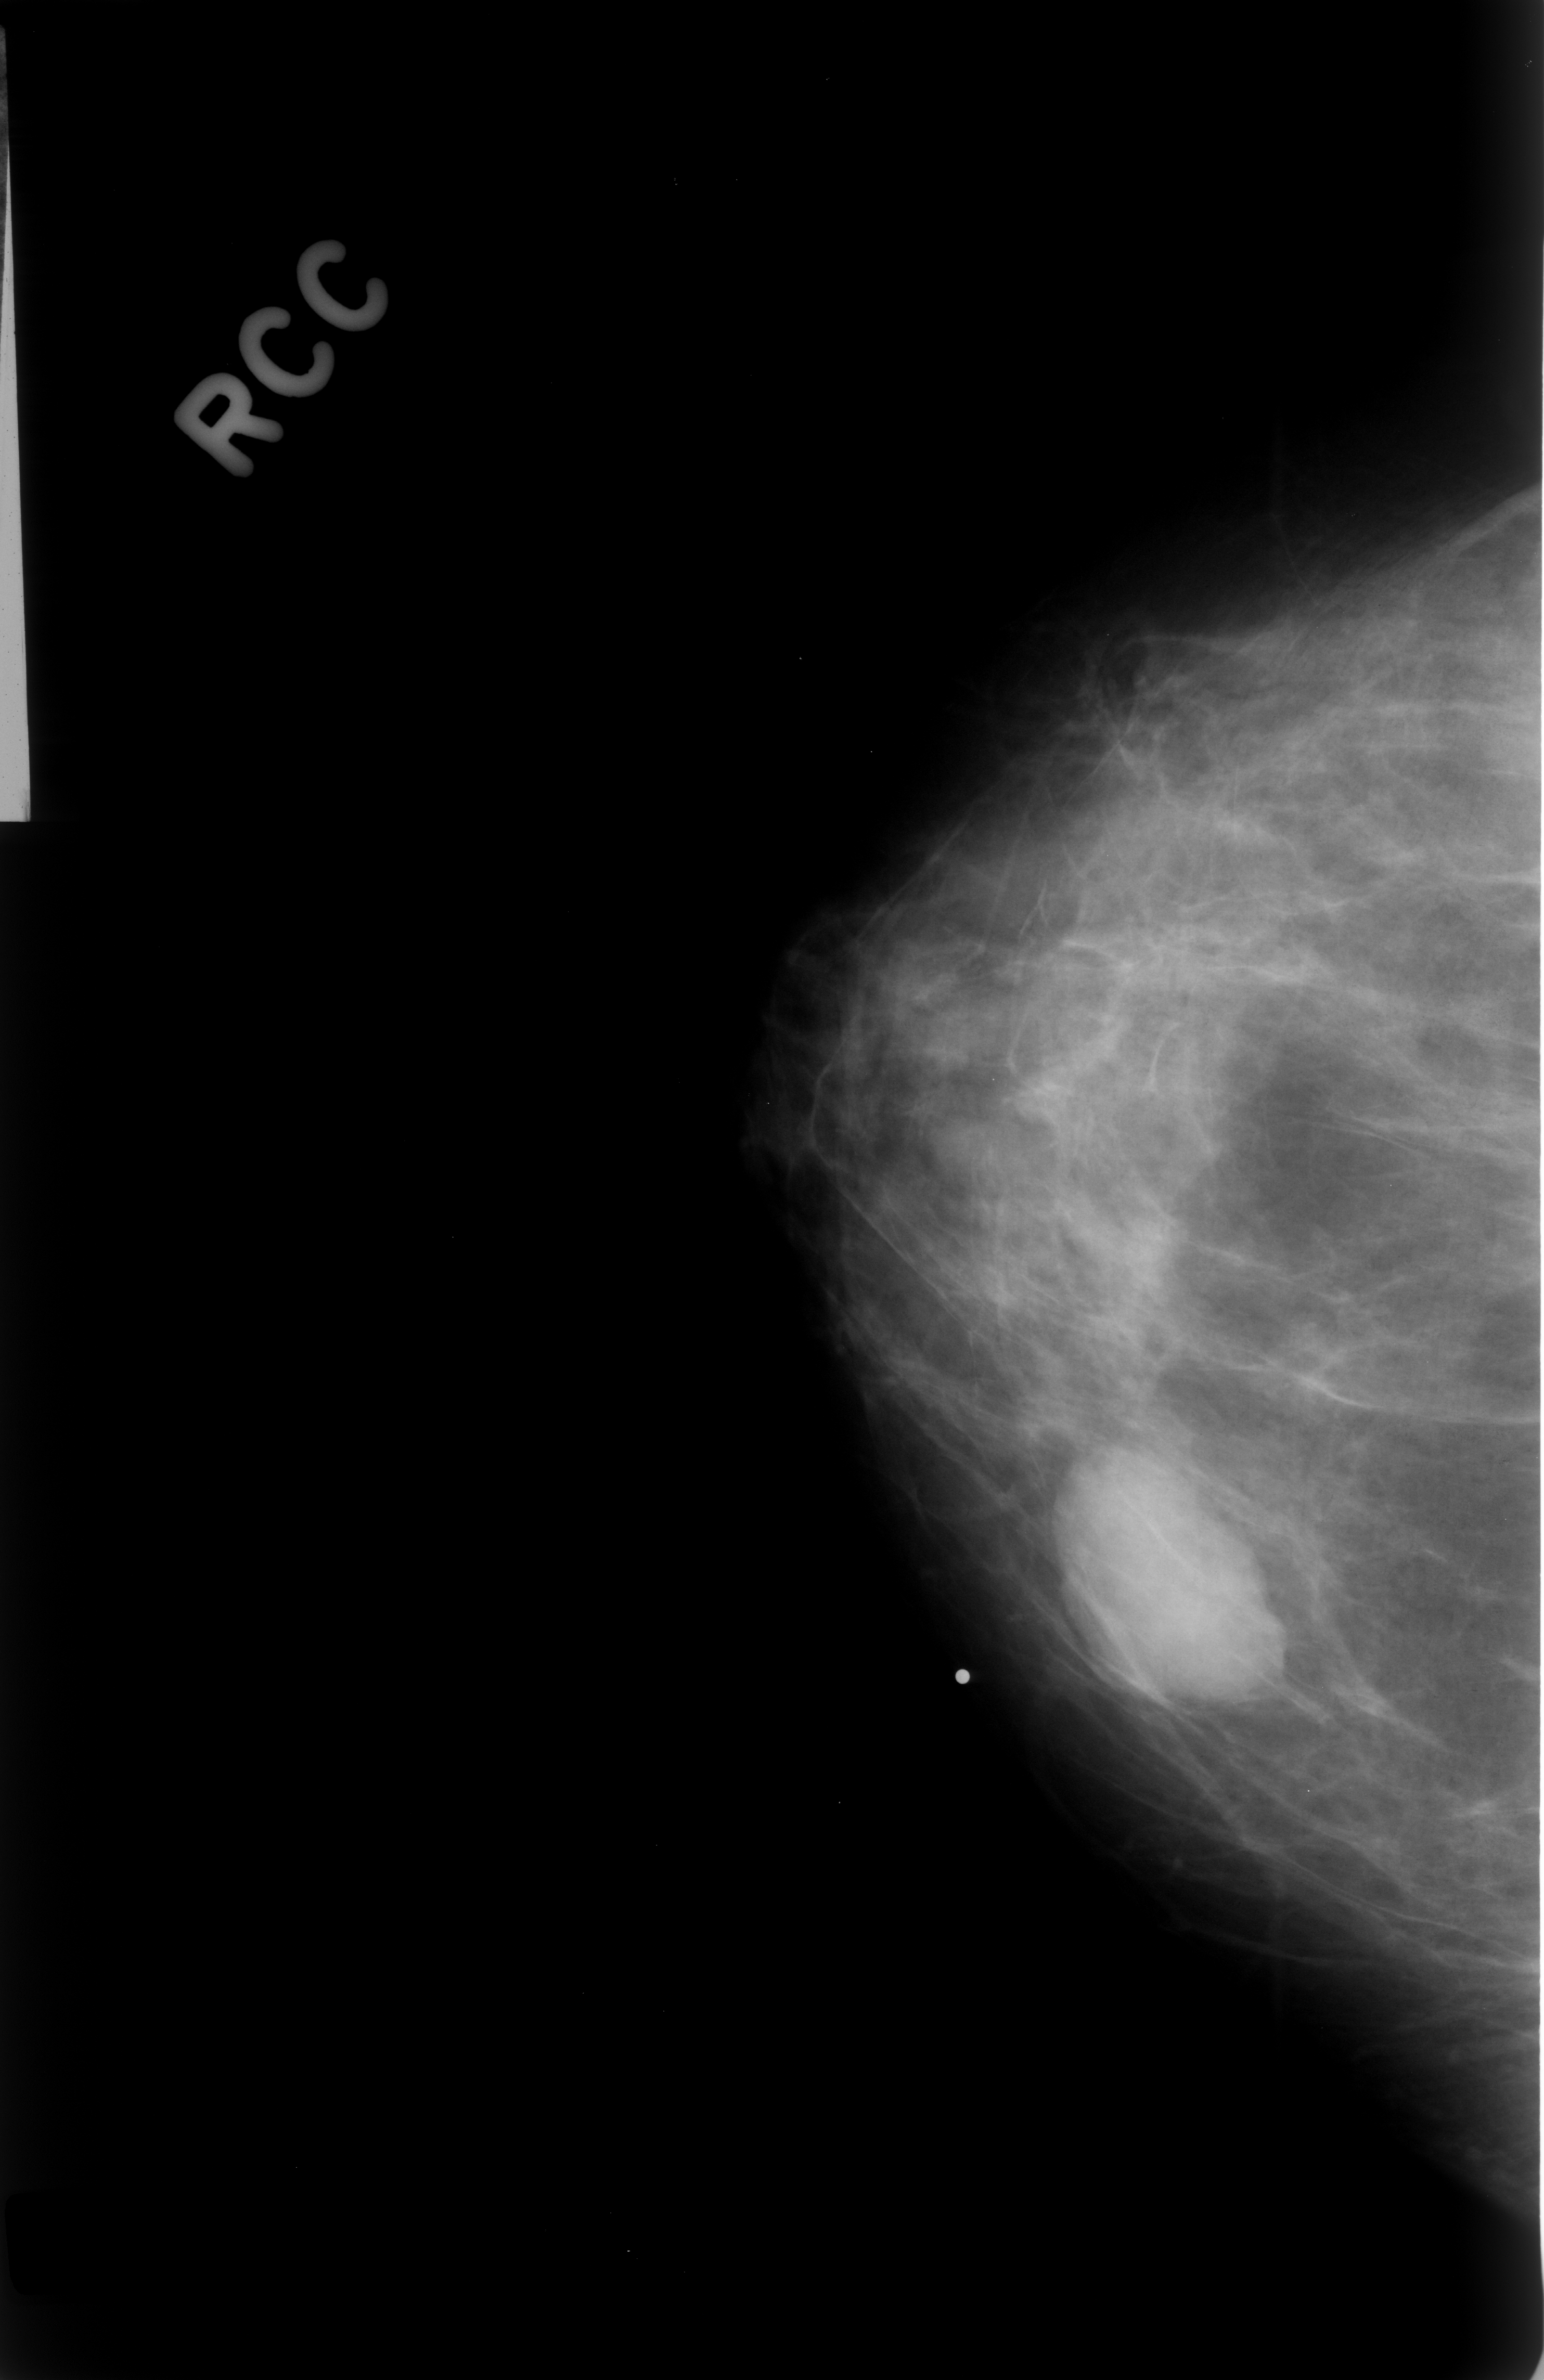
Mammogram (digitized film), right breast, craniocaudal (CC) view, BI-RADS breast density category 2 (scale 1–4).
Mass, shape oval, margins circumscribed; BI-RADS assessment category 3; pathology result (as recorded, not read from the image): benign.